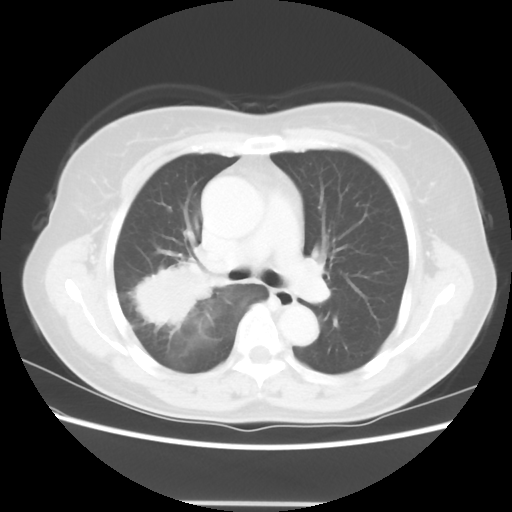
Chest CT, one axial slice. Position 37 of 56 along the scan axis. 120 kVp. Lung window (W 1500 / L -600 HU). 5 mm slice thickness. 512 × 512 image matrix, field of view 360 × 360 mm. Female patient, age 55 years. Case-level facts recorded for this patient, not image findings: clinical TNM (as recorded): T2 N1 M0; histopathological grade: G2-3.
Outlined on this slice (rectangle marked by the reading radiologist):
- lung tumour (recorded histology: adenocarcinoma): bounding box [x1, y1, x2, y2] px = [122, 258, 223, 340]